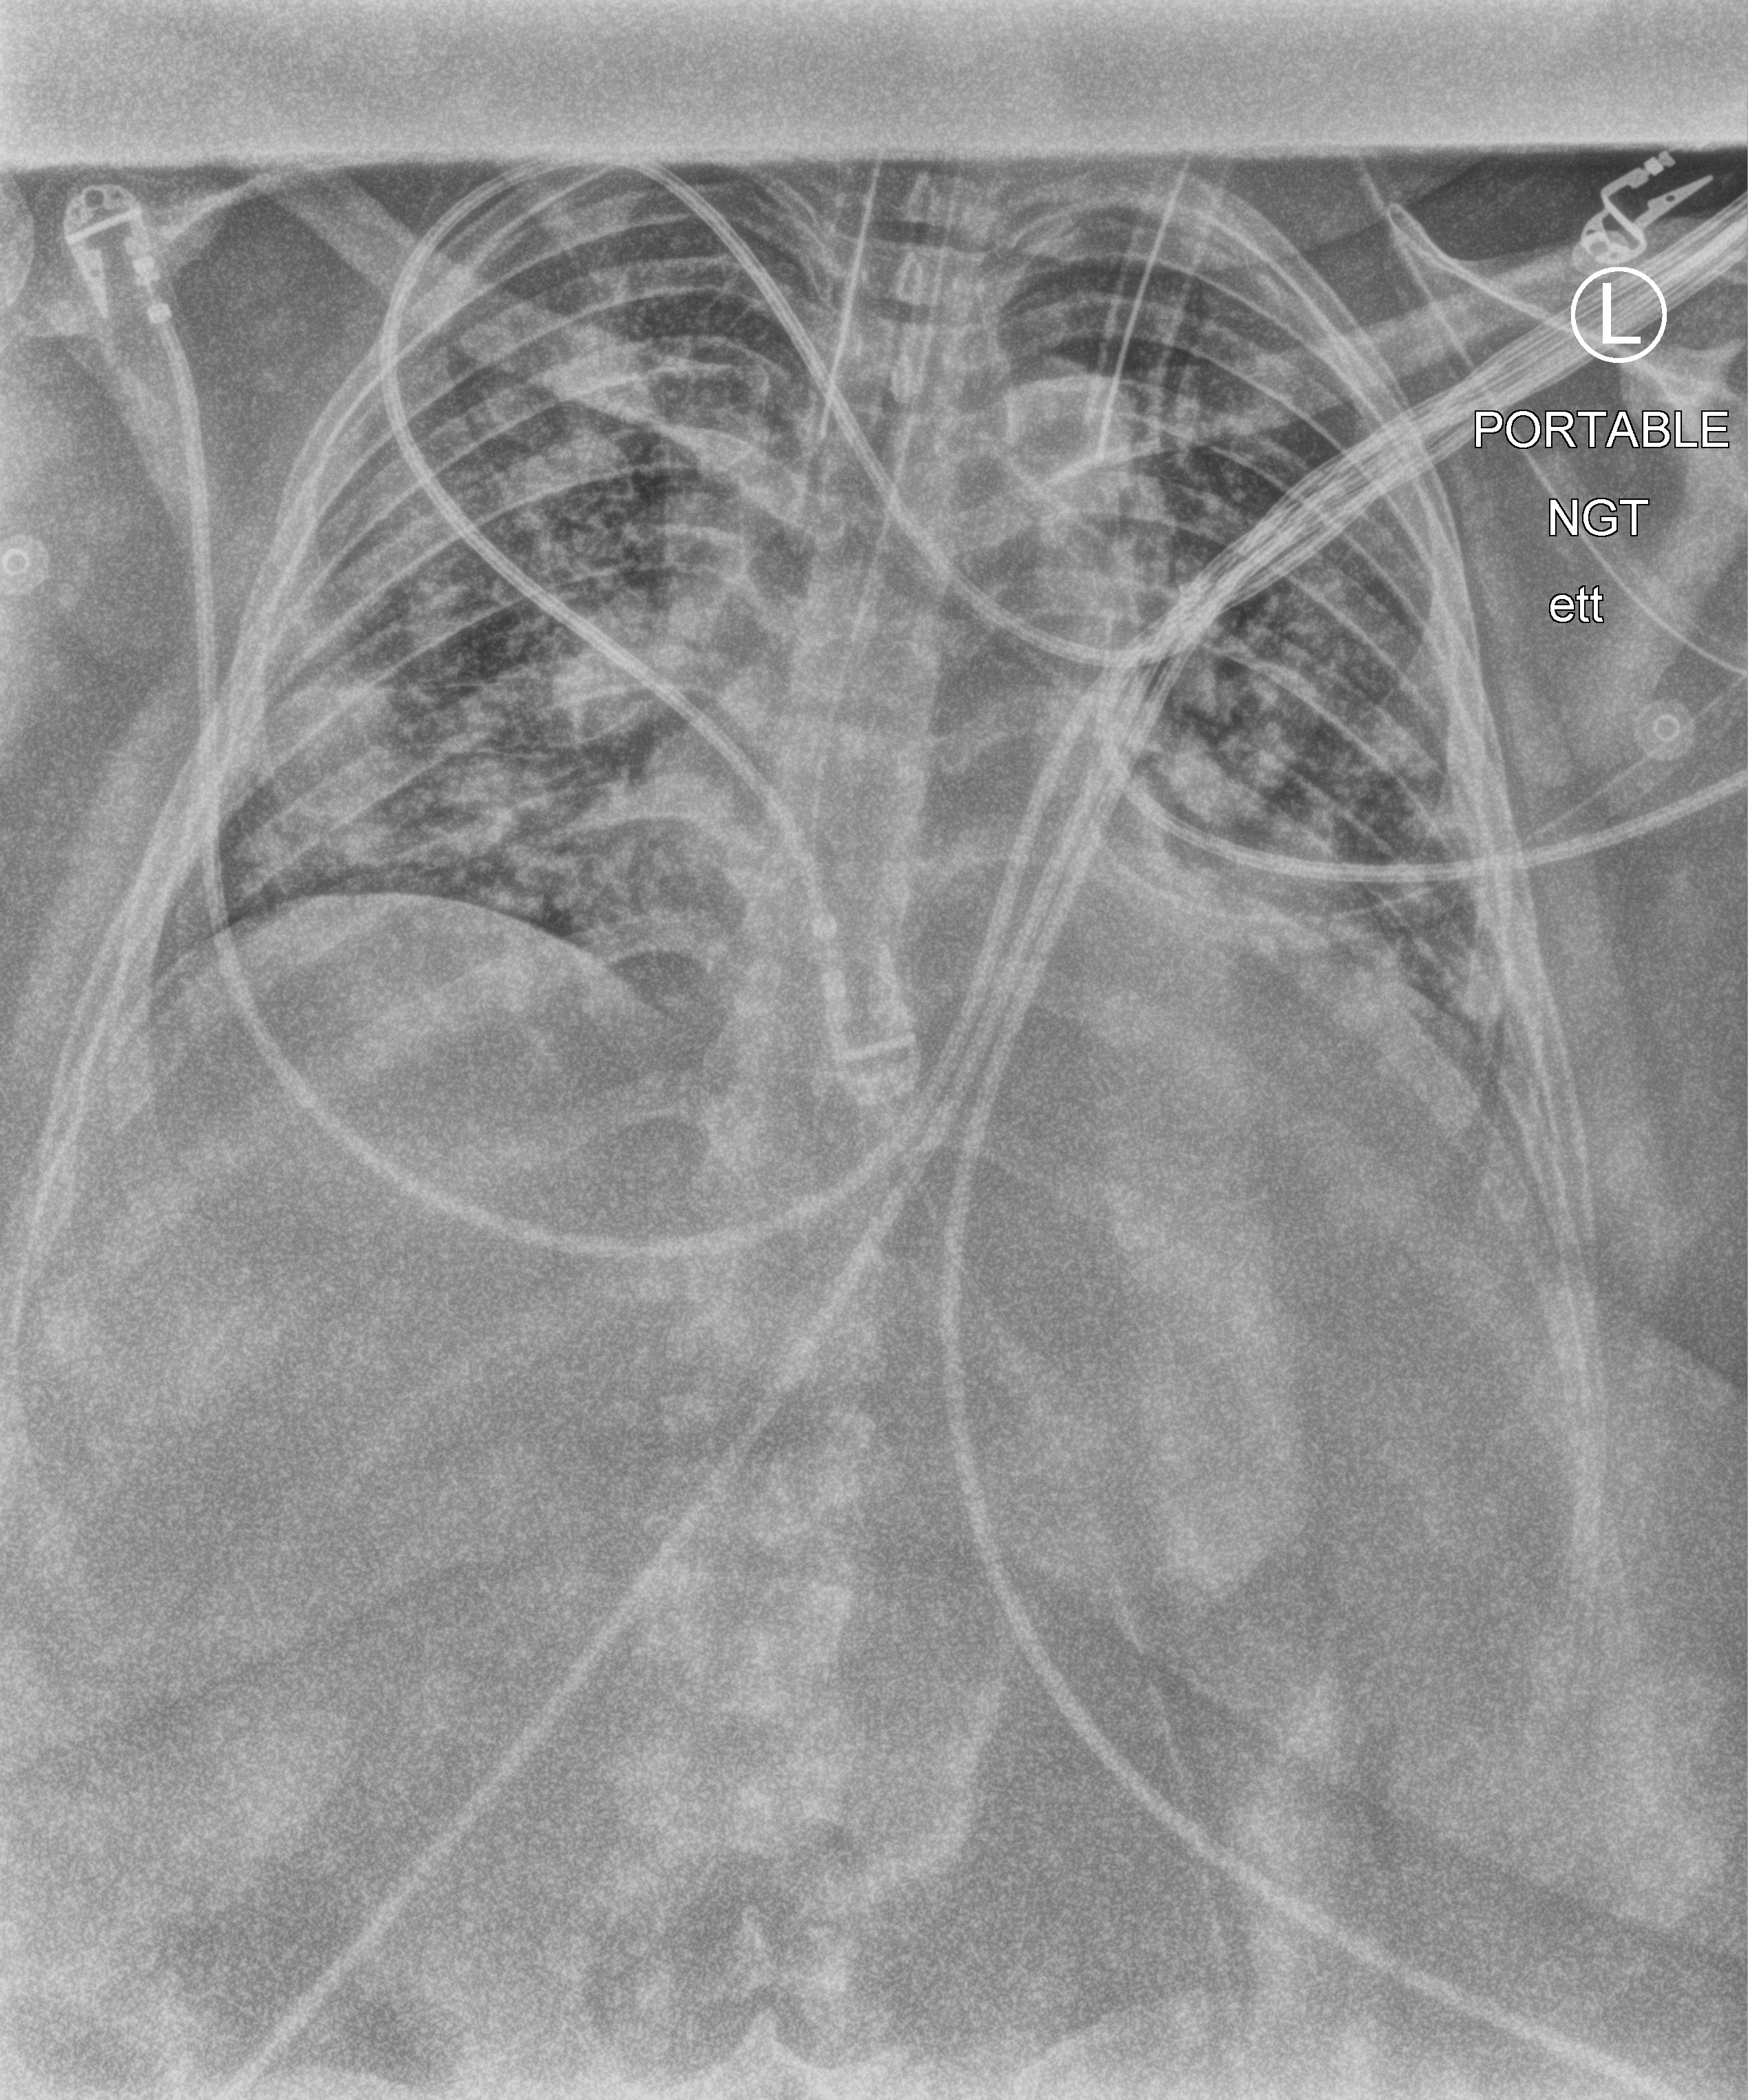
Portable chest radiograph, anteroposterior (AP) projection. Female patient hospitalised with COVID-19, age 18–59 years.
Admission-level facts for this patient (not findings on this image; timing relative to this image not recorded): diabetes (admission record): yes.